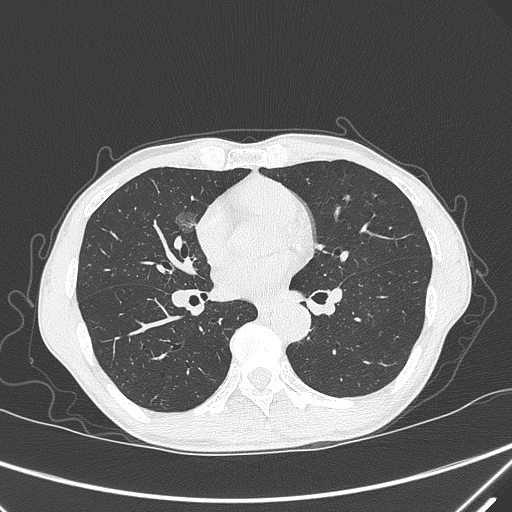
Chest CT, one axial slice; slice 164 of 339 in the series (ordered by position); 120 kVp; lung window (W 1500 / L -600 HU); 1 mm slice thickness; 512 × 512 image matrix. Male patient, age 67 years. From the clinical record (not read from this slice): clinical TNM (as recorded): T1c N0 M0; histopathological grade: G1-2.
Annotated regions visible in this slice (bounding box drawn by a radiologist):
- lung tumour (recorded histology: adenocarcinoma): bounding box (x1, y1, x2, y2) in pixels: (170, 203, 203, 239)